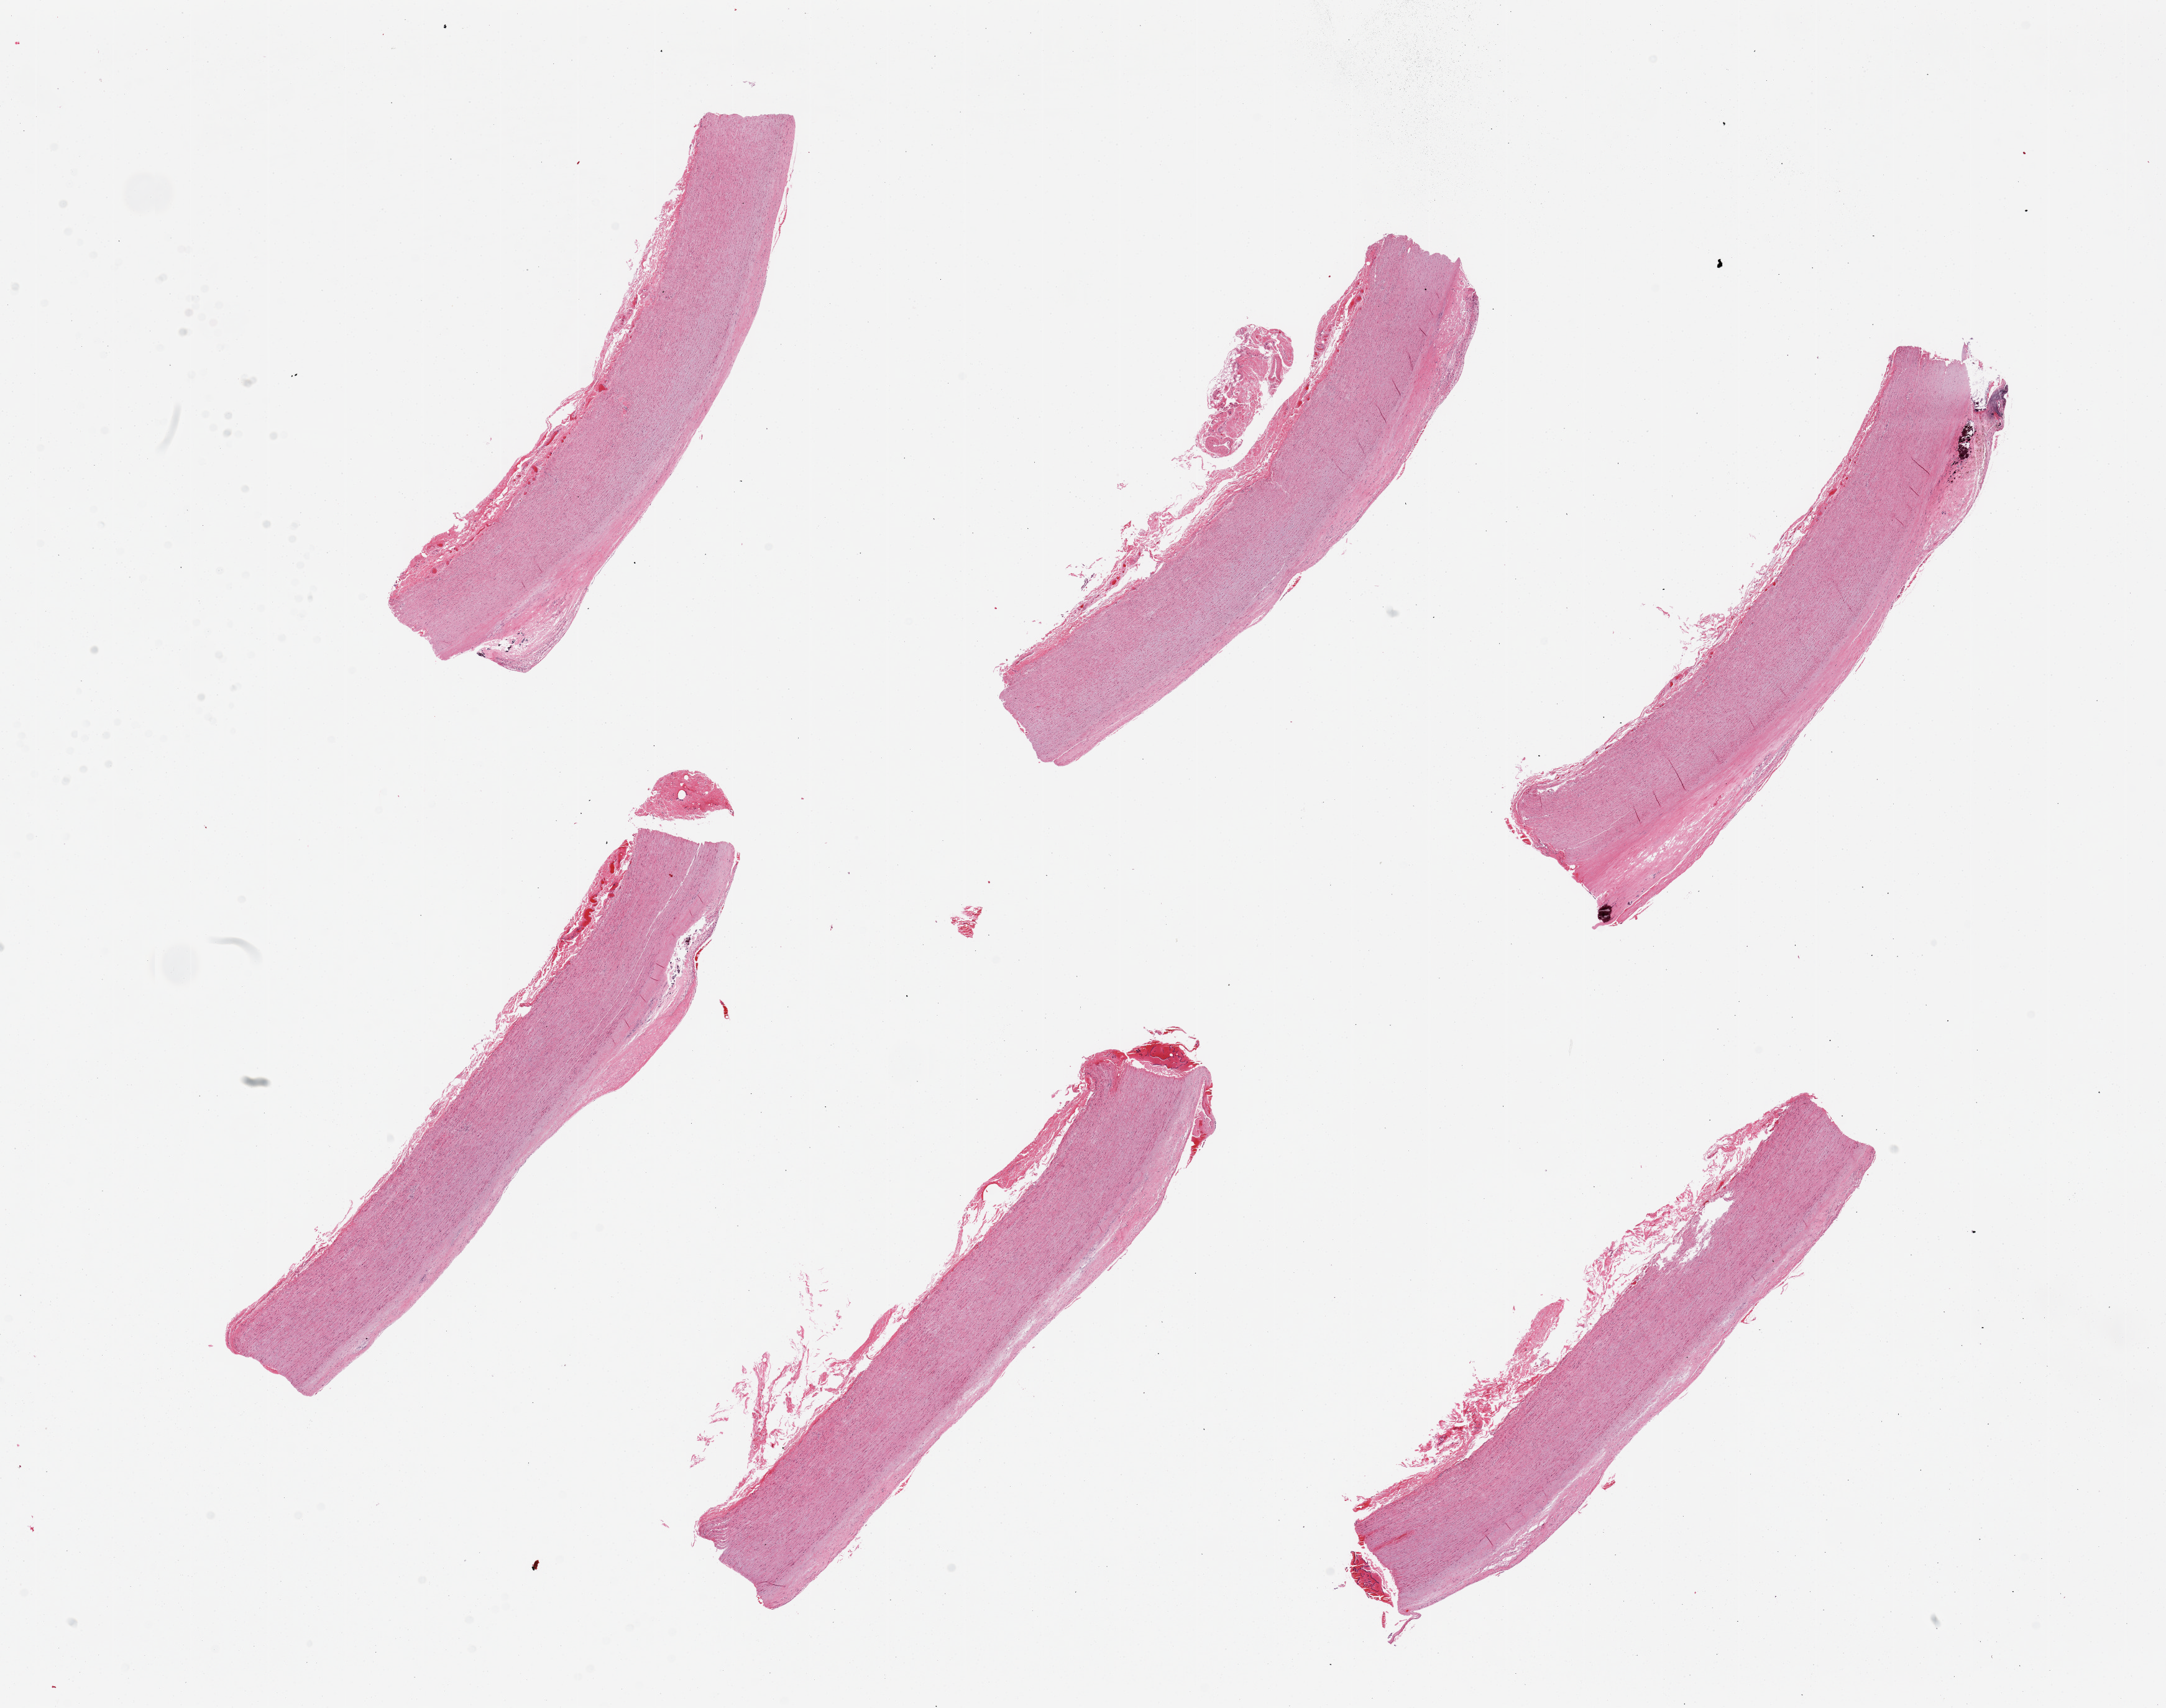
Hematoxylin and eosin (H&E) whole-slide image — low-resolution overview of the scanned area, about 27.6 x 21.7 mm, PAXgene-fixed, paraffin-embedded tissue, target tissue: aorta, tissue donor sample. Donor sex: female.
• pathologist's review note for this sample: 6 pieces; focally calcified atherosclerotic plaques; well trimmed